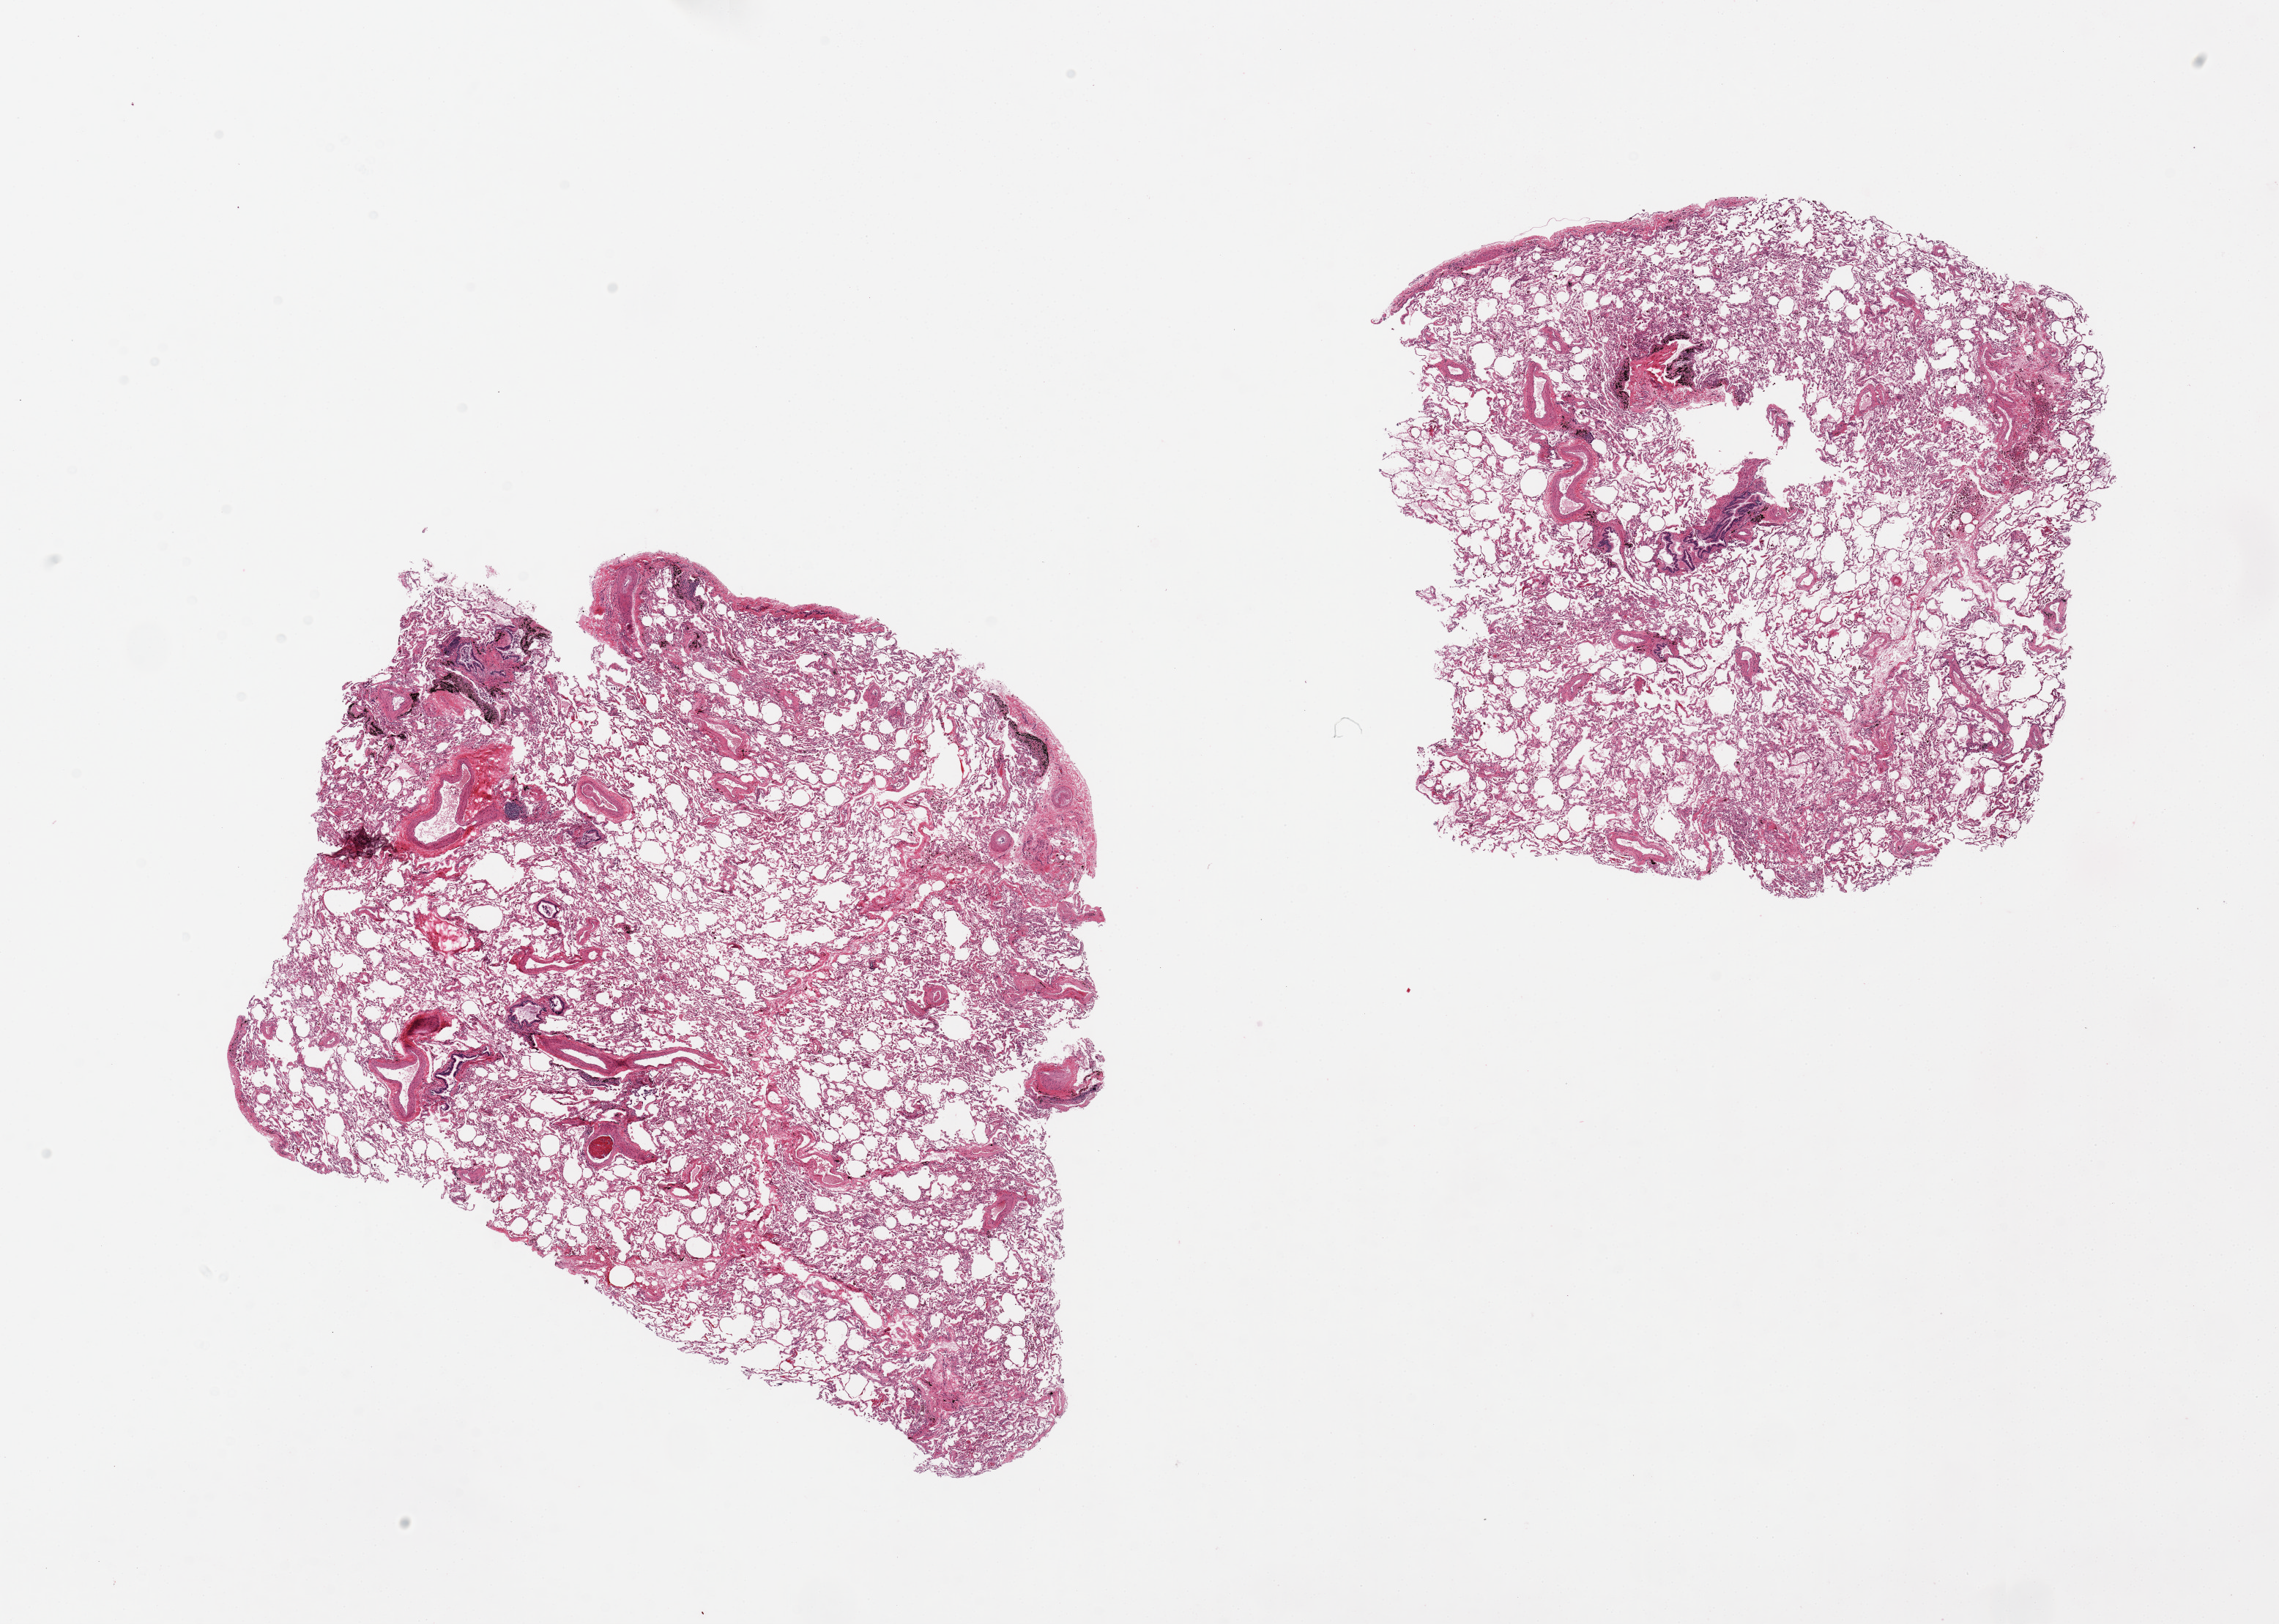
H&E whole-slide image, shown as a low-resolution overview of the whole scanned area (about 24.6 x 17.5 mm, acquisition: 20x scan); PAXgene-fixed paraffin-embedded (PFPE) section; section of lung (target tissue); donor tissue sample. Donor sex: male.
Pathologist's review note for this sample: 2 pieces; few collections of chronic inflammatory cells and numerous hemosiderin-laden macrophages.